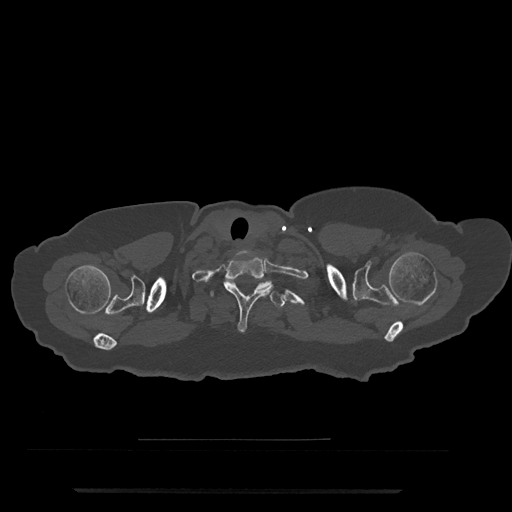
CT including the spine, one axial slice; slice 703 of 797 in the series (ordered by position); reconstruction kernel Br40s/3; 120 kVp; bone window (W 1800 / L 400 HU); 512 × 512 image matrix, field of view 440 × 440 mm. Patient: female, 51 years. Case-level facts recorded for this patient, not image findings: primary cancer: neuro.
Structures marked on this image (semi-automatically segmented with operator editing):
- T1 vertebra: bounding box [x1, y1, x2, y2] px = [223, 257, 294, 333]
- T2 vertebra: [210, 279, 285, 308]